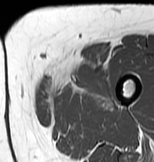
MRI of an extremity soft-tissue mass, one axial slice. Slice 14 of 83 in the series (ordered by position). MR volume resampled by the dataset authors to the PET/CT grid (not the native acquisition matrix). 3.27 mm slice thickness. 154 × 162 image matrix, field of view 150 × 158 mm. Female patient. Case-level facts recorded for this patient, not image findings: histological type: myxofibrosarcoma; grade: intermediate; site of the primary tumour: left thigh.
Outlined on this slice (expert contour drawn on MRI and transferred to this co-registered scan by the dataset authors):
- gross tumour volume including surrounding oedema: bounding box [x1, y1, x2, y2] px = [39, 66, 114, 108]
- gross tumour volume (mass): [74, 66, 98, 76]